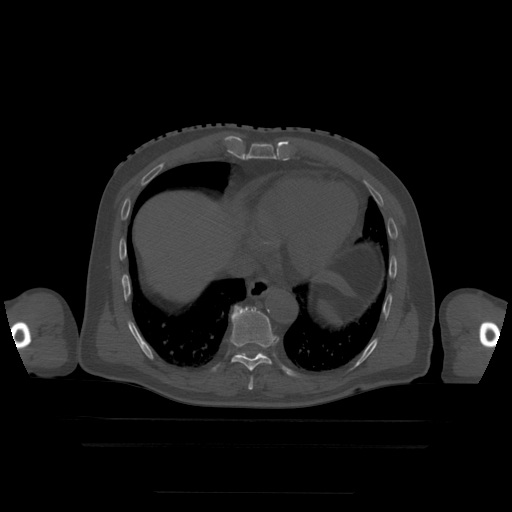
CT including the spine, one axial slice. Position 259 of 522 along the scan axis. Bone window (W 1800 / L 400 HU). 512 × 512 image matrix, field of view 436 × 436 mm. Patient age 68 years. Case-level facts recorded for this patient, not image findings: primary cancer: urothelial.
Outlined on this slice (semi-automatic segmentation, software-assisted and operator-edited):
- T10 vertebra: box from (x=257, y=353) to (x=265, y=356) px
- T8 vertebra: (x=249, y=378)–(x=254, y=390)
- T9 vertebra: (x=230, y=306)–(x=277, y=372)